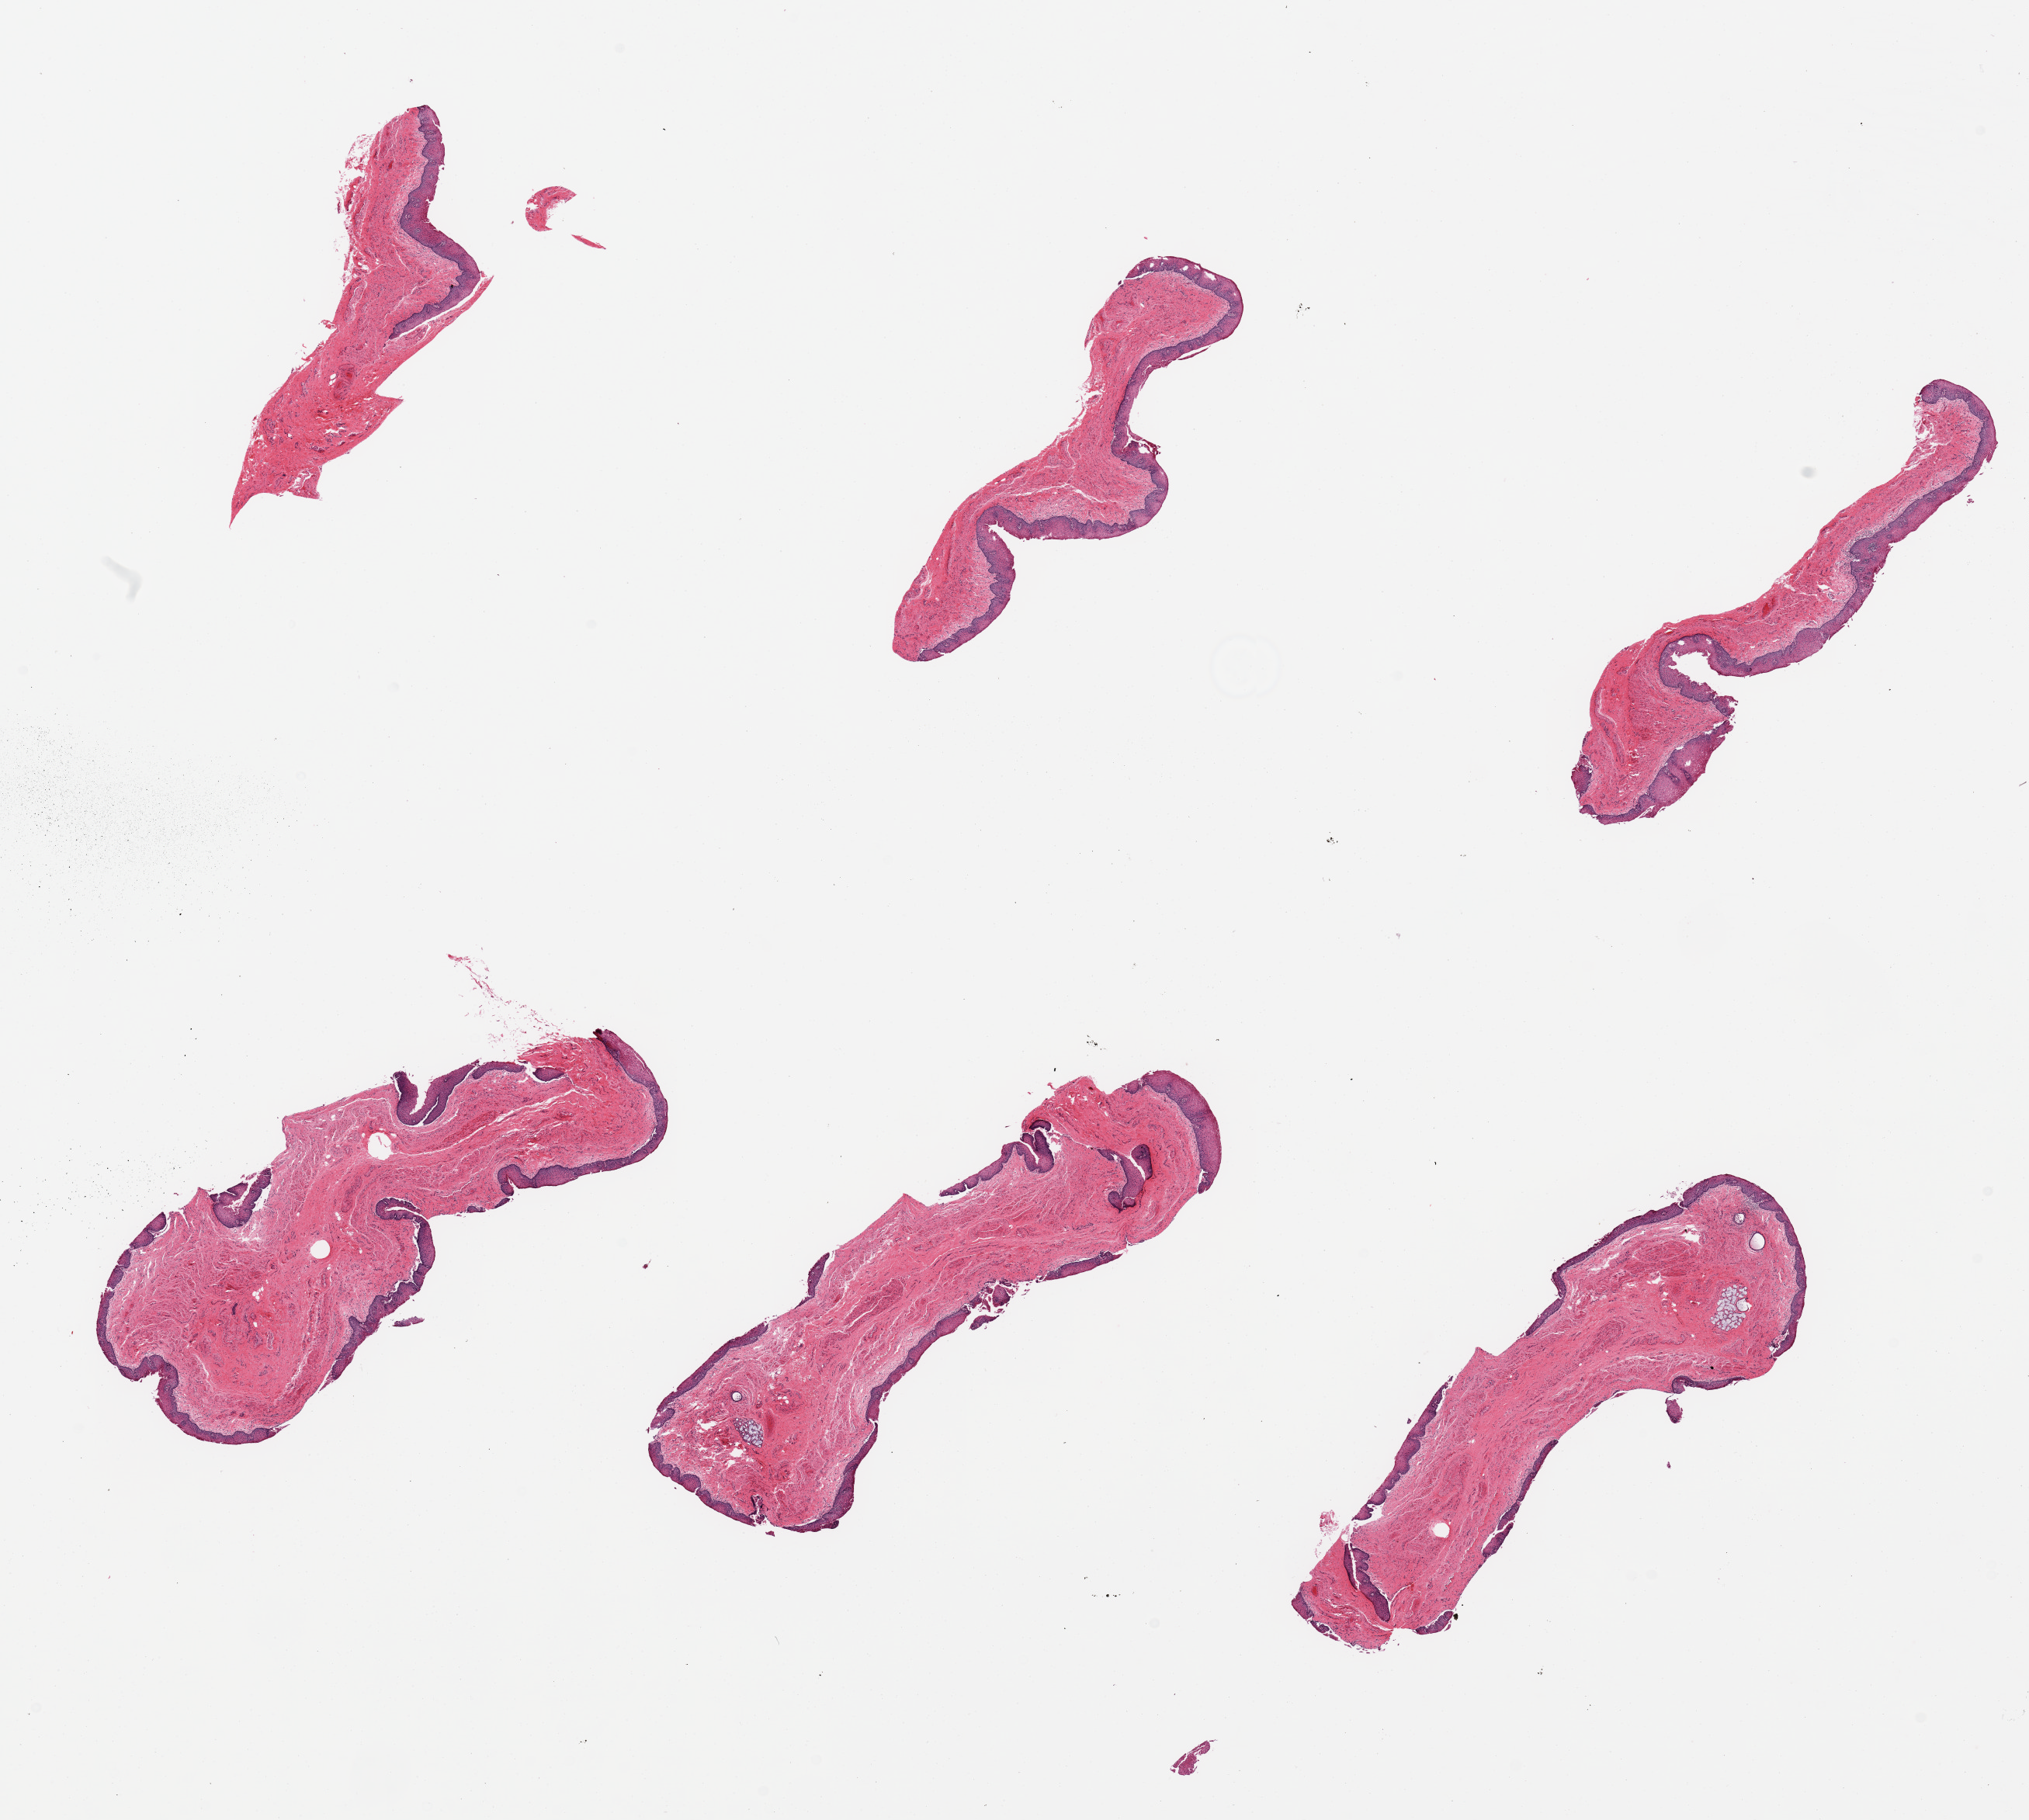
Digitized hematoxylin and eosin (H&E)-stained section, a low-resolution overview of the entire scanned area, about 20.7 x 18.5 mm (from a 20x scan); PAXgene-fixed paraffin-embedded (PFPE) section; section of esophageal mucous membrane (target tissue); donor tissue sample. Donor sex: male.
* pathologist's review note for this sample: 6 pieces, Squamous mucosa is ~0.2mm, ~10% thickness